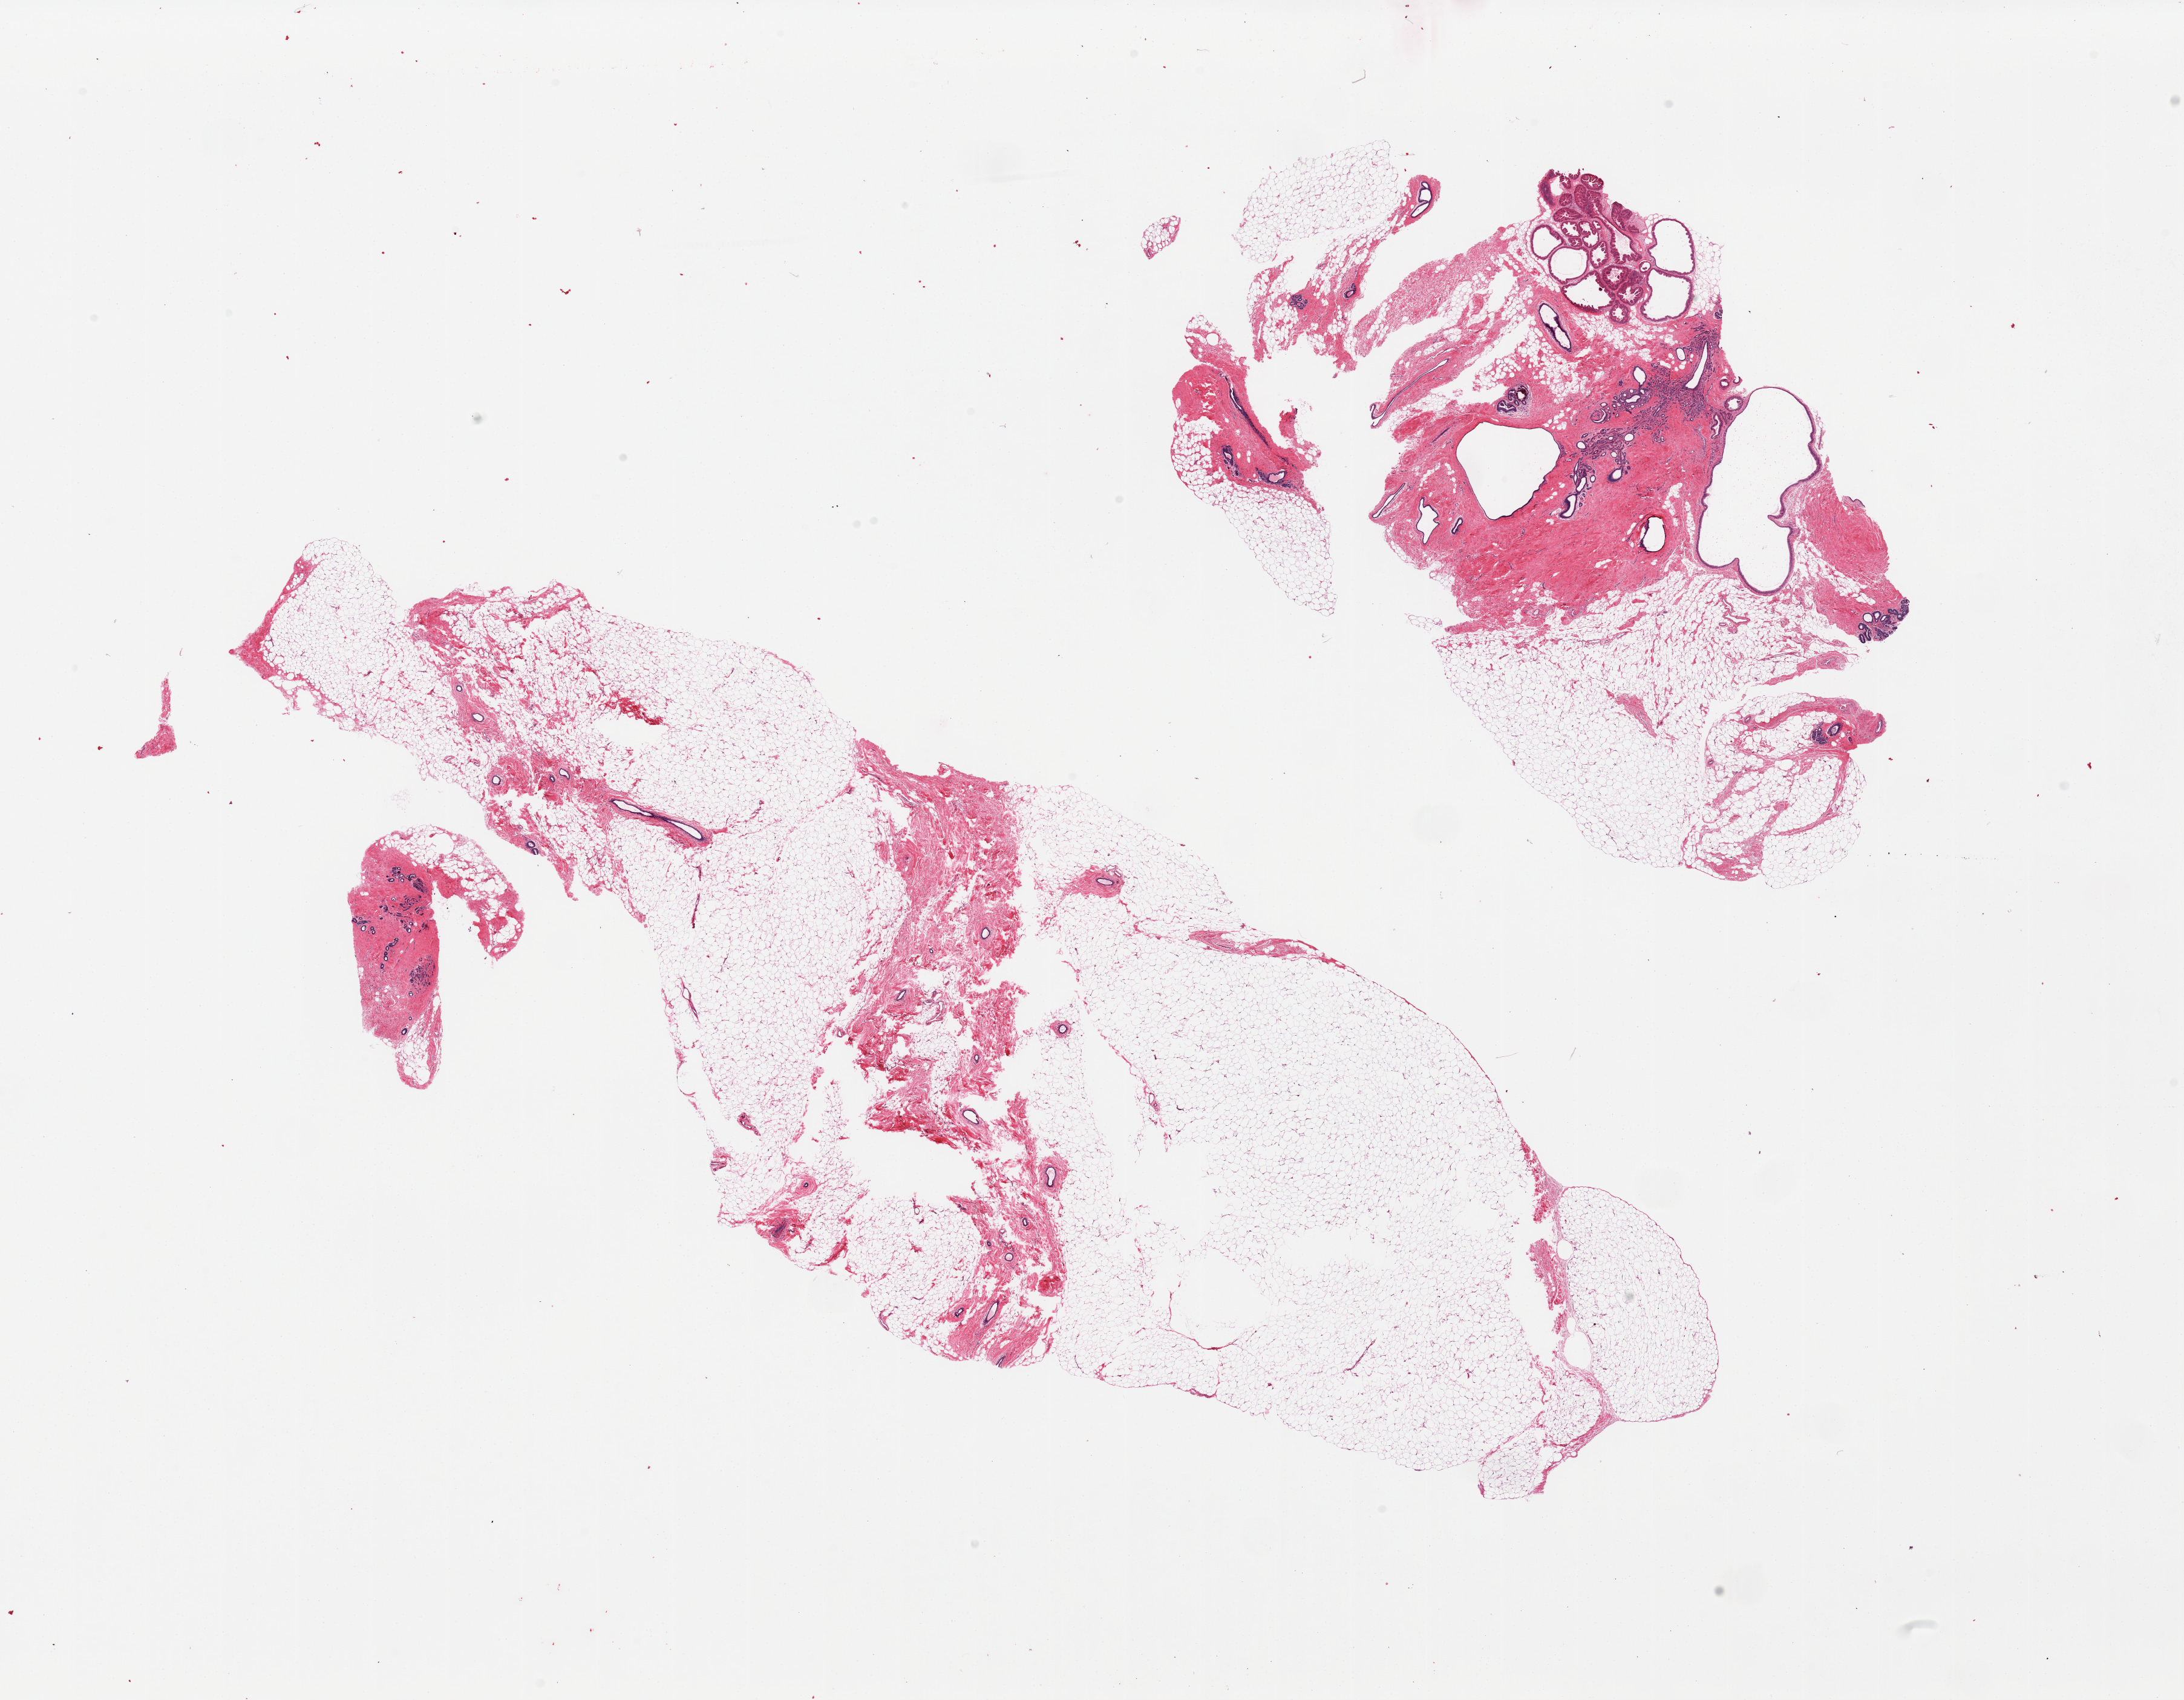
Whole-slide image, haematoxylin and eosin stain — a low-resolution overview of the entire scanned area, about 28.5 x 22.2 mm; PAXgene-fixed, paraffin-embedded tissue; target tissue: breast; tissue donor sample. Donor sex: female.
Reviewer comment on this tissue sample: 2 pieces, one with prominent fibrocystic change, prominent focus of apocrine metaplasia.